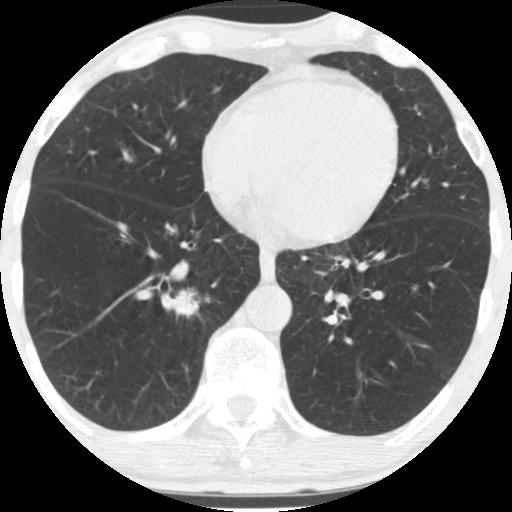
Low-dose screening chest CT, one axial slice; position 58 of 170 along the scan axis; 120 kVp; lung window (W 1500 / L -600 HU); 2.5 mm slice thickness; 512 × 512 image matrix, field of view 290 × 290 mm.
Outlined on this slice (expert manual segmentation):
- lesion 1 (tumor, lower lobe of right lung): bounding box (x1, y1, x2, y2) in pixels: (174, 292, 198, 315)